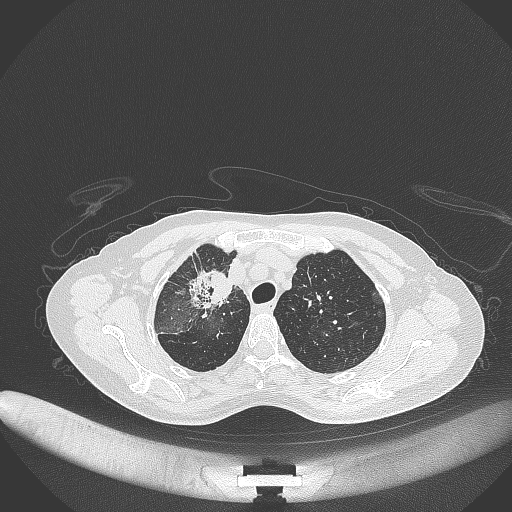
Chest CT, one axial slice. Position 258 of 284 along the scan axis. 120 kVp. Lung window (W 1500 / L -600 HU). 1 mm slice thickness. 512 × 512 image matrix, field of view 400 × 400 mm. Female patient, age 59 years. Case-level facts recorded for this patient, not image findings: clinical TNM (as recorded): T3 N0 M0; histopathological grade: G1.
Outlined on this slice (rectangle marked by the reading radiologist):
- lung tumour (recorded histology: adenocarcinoma): bounding box <186,271,233,308> (left, top, right, bottom; pixels)